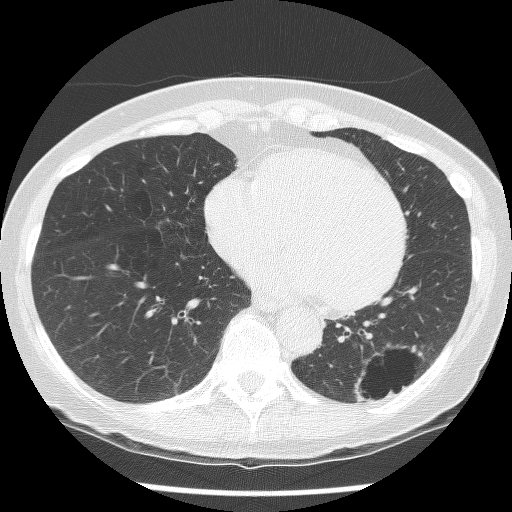
Axial slice from a low-dose chest CT screening exam; second screening round (one year after baseline); lung window (W 1500 / L -600 HU); 2.5 mm slice thickness; lung (sharp) reconstruction kernel (BONE); 120 kVp. Female, age 61 years at enrolment. Current smoker at enrolment.
Expert reader's lesion annotation, bounding box [x1, y1, x2, y2] px = [333, 330, 435, 417]. The screening reader recorded 2 non-calcified nodules or masses ≥4 mm on this exam; which of them this box marks is not recorded. Official screen result: positive, no significant change: stable abnormalities potentially related to lung cancer, unchanged since the prior screening exam. Later outcome: lung cancer diagnosed 585 days after this screen (after the third annual screen) — non-small cell carcinoma, left lower lobe, poorly differentiated (G3), stage IB (AJCC 6th edition), 100 mm at pathology.